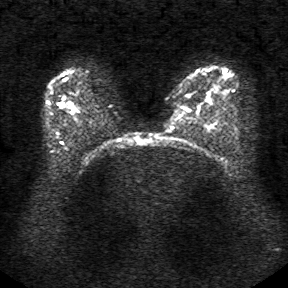
Breast MRI, one axial slice. Position 24 of 34 along the scan axis. Diffusion-weighted series; image 2 of 4 stored at this slice position (different b-values; order by instance number). 1.5 T. 288 × 288 image matrix, field of view 340 × 340 mm. Female patient.
Structures marked on this image (expert manual segmentation):
- tumour on diffusion-weighted imaging: bounding box (x1, y1, x2, y2) in pixels: (65, 104, 71, 109)